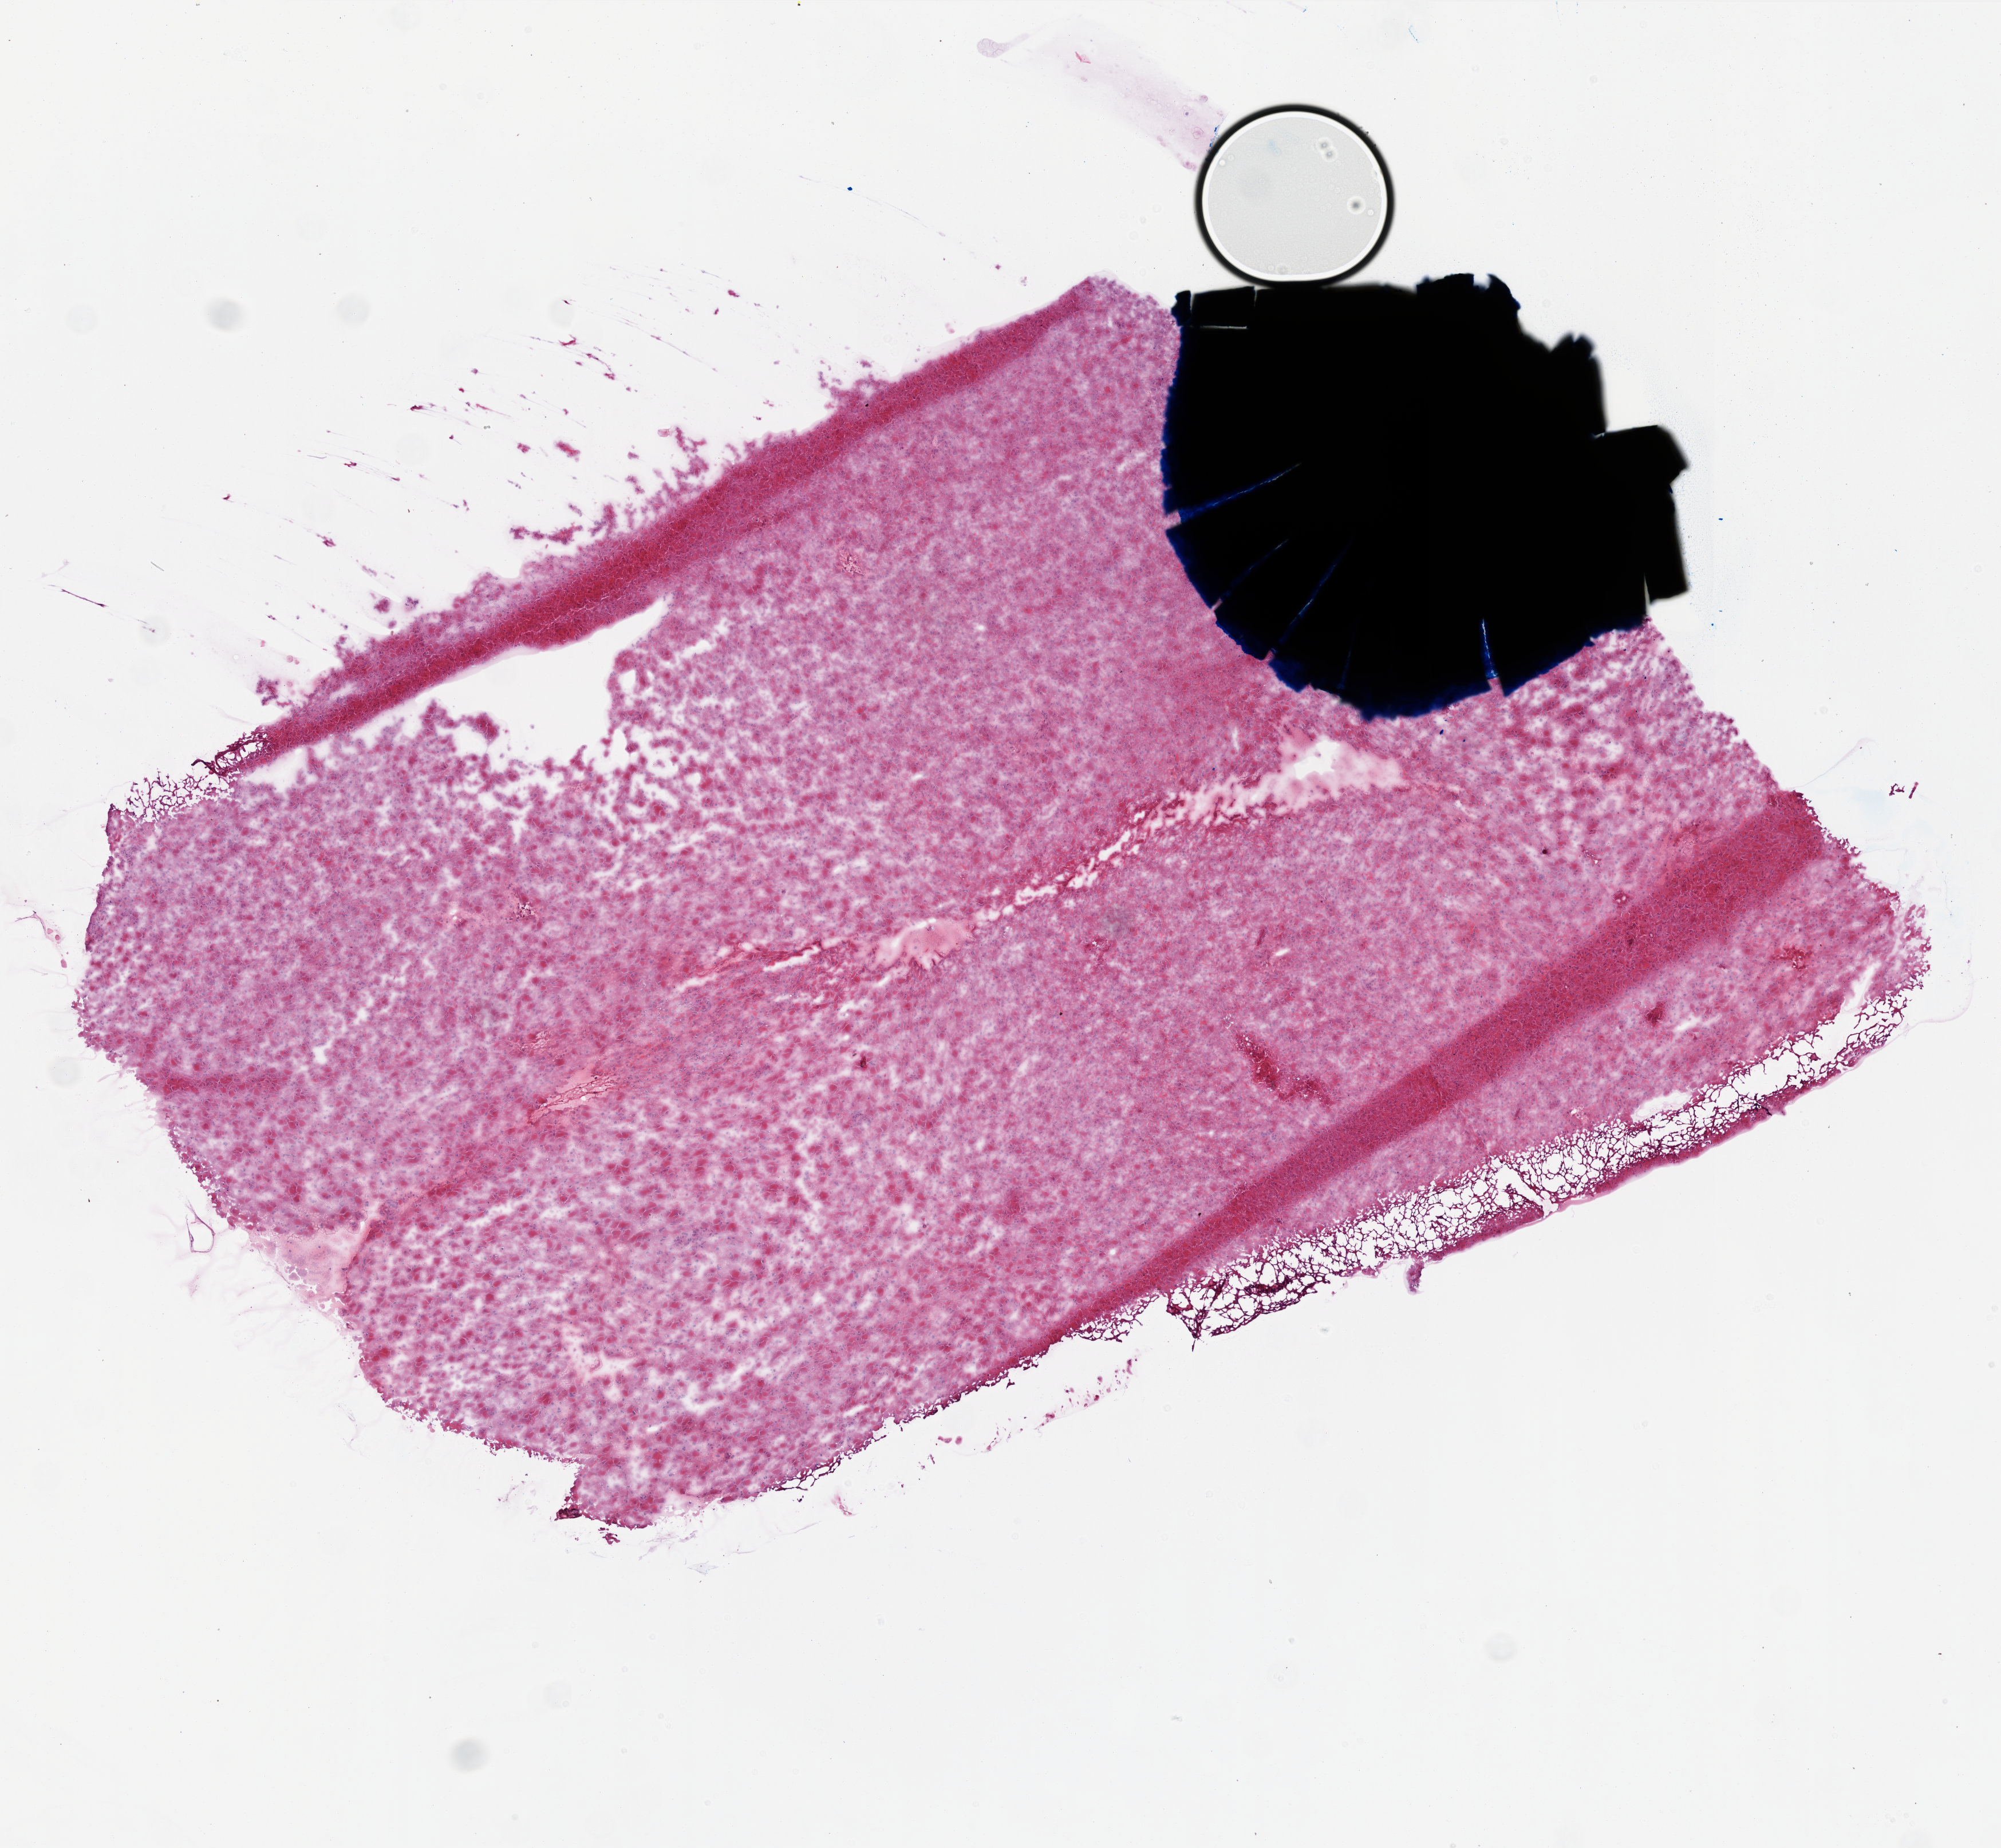
Whole-slide histology image, H&E-stained — whole scanned area (about 7.0 x 6.5 mm, acquisition: 20x scan) shown as a low-resolution overview, frozen section from the top of the tissue portion, brain, primary tumour sample. Female patient; age at initial diagnosis 74 years. Slide review estimates, as recorded: tumour cells 100%, tumour nuclei 100%, normal cells 0%, stromal cells 0%, necrosis 0%.
• diagnosis: Glioblastoma